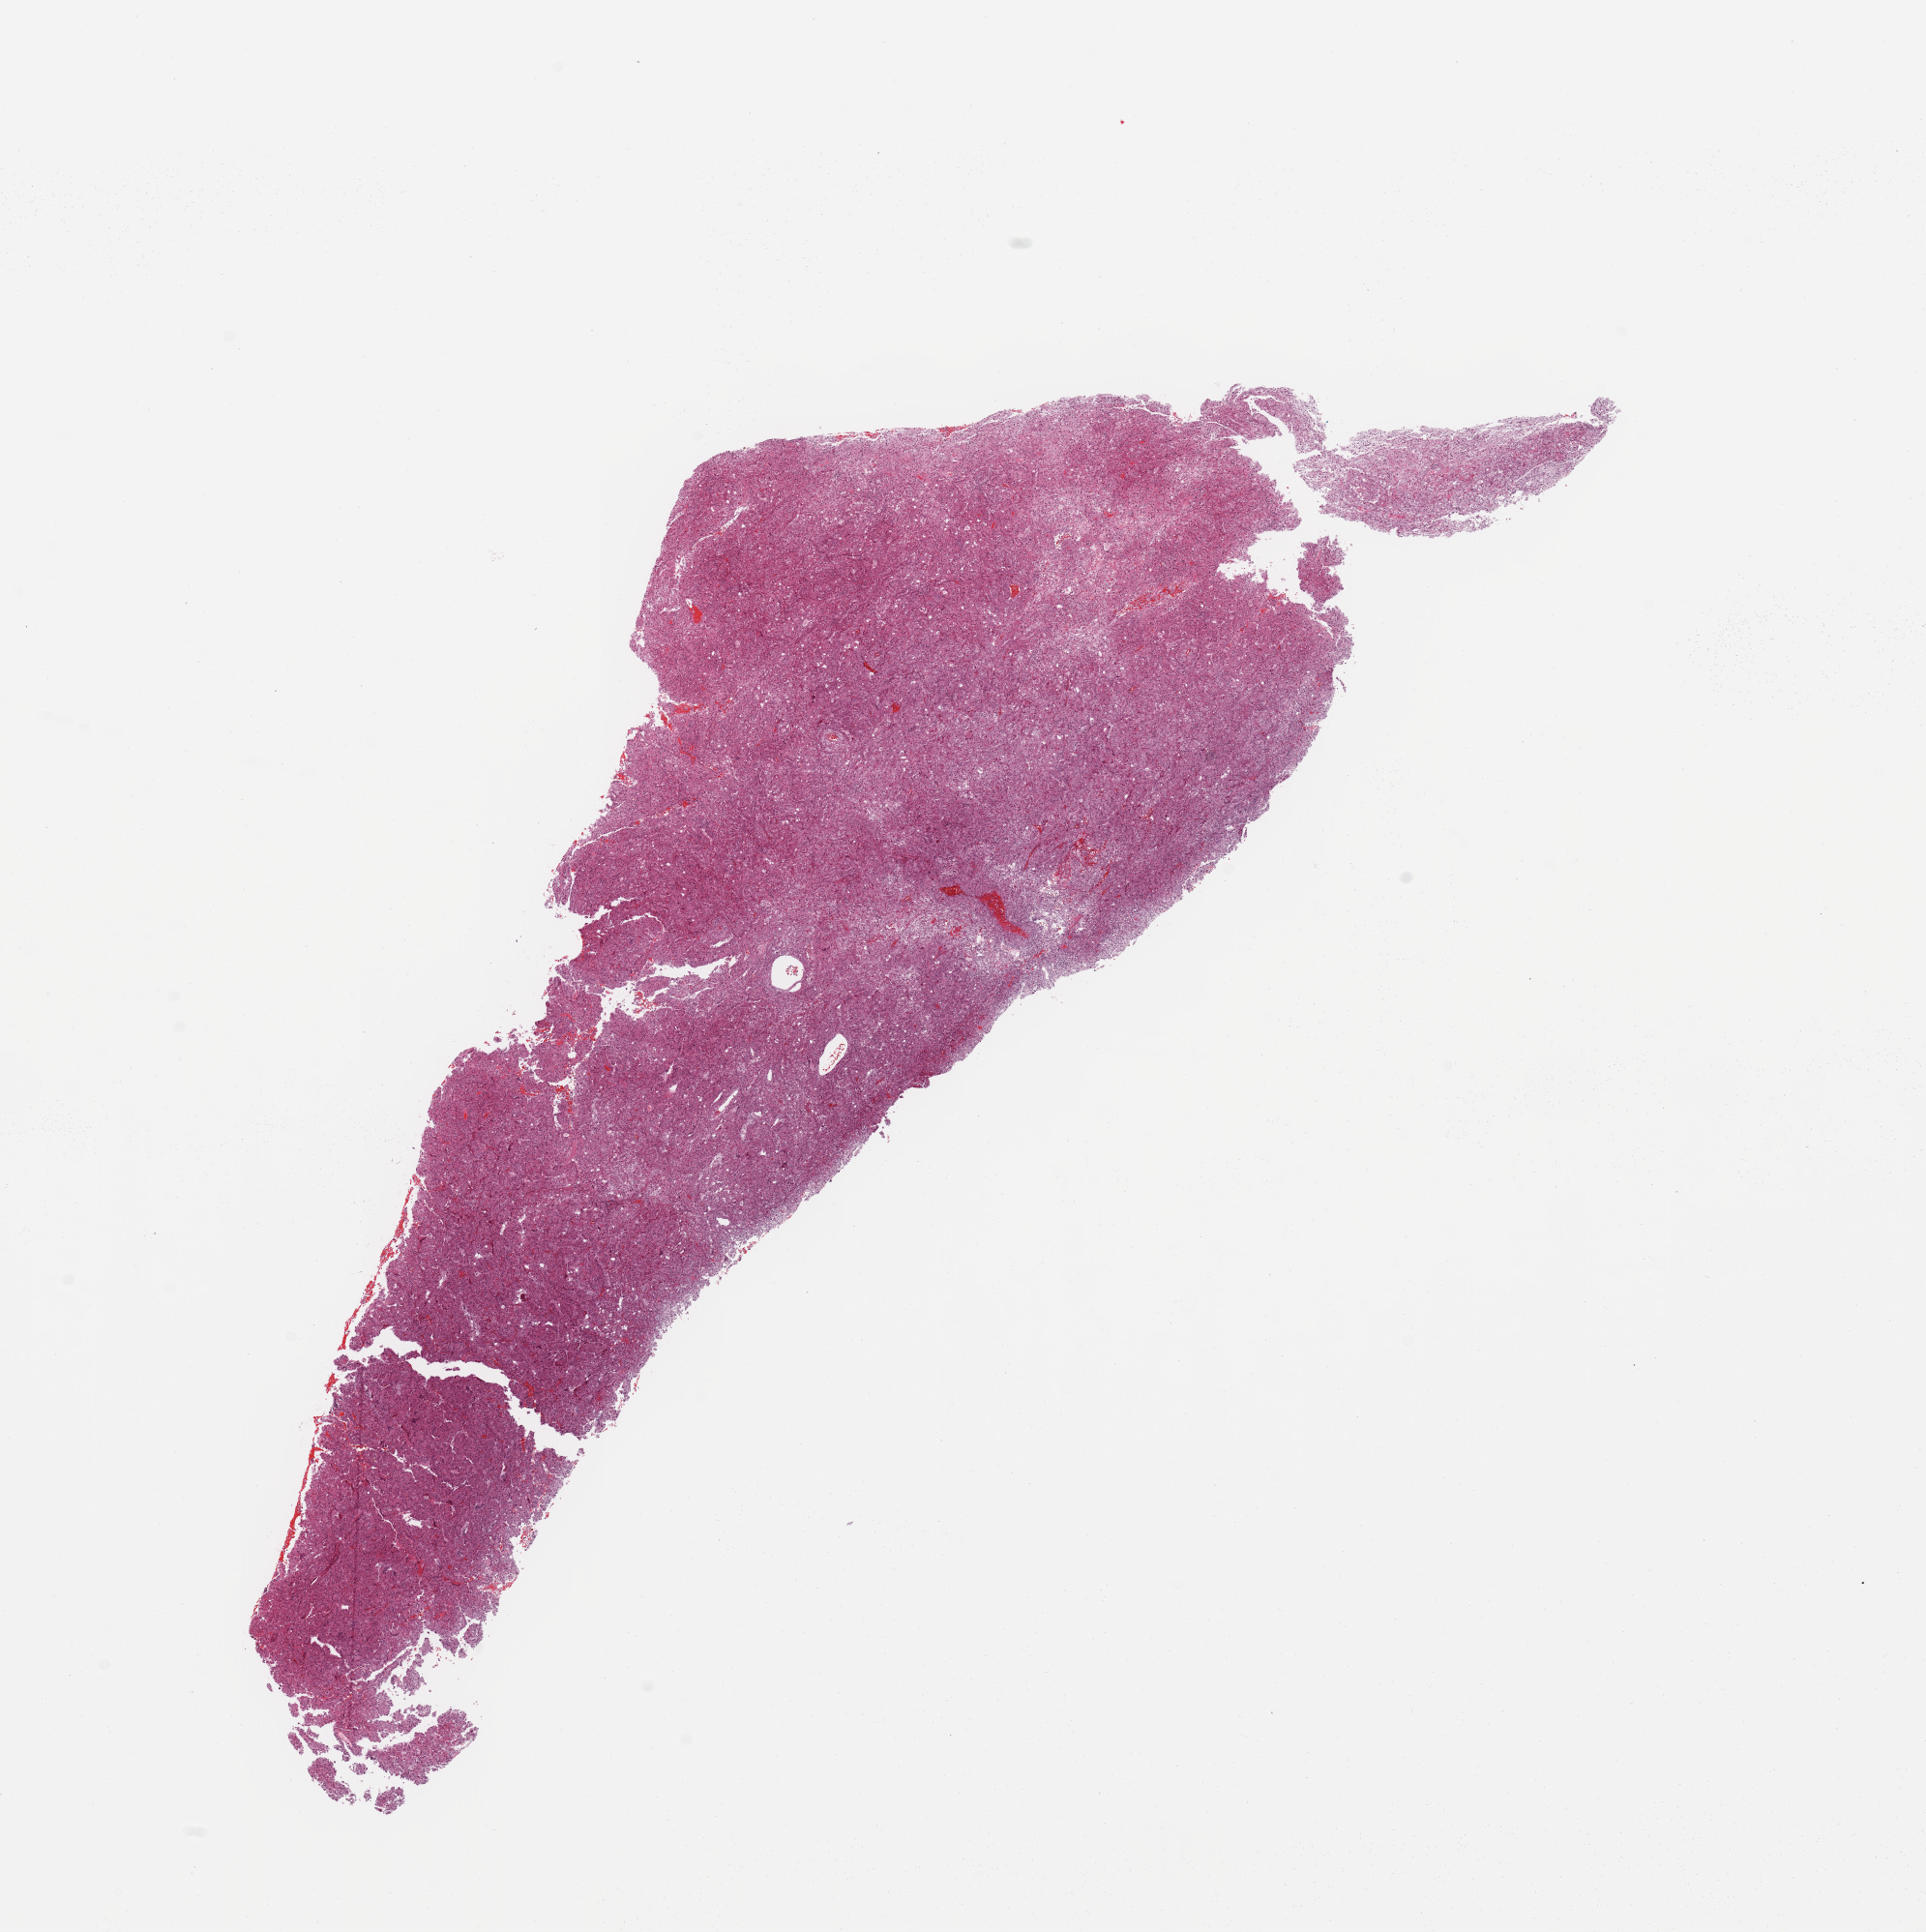
H&E whole-slide image — whole scanned area (about 15.8 x 15.8 mm, acquisition: 20x scan) shown as a low-resolution overview. Kidney, tumour tissue. 68-year-old female patient. Histologic grade: G4 (undifferentiated).
- diagnosis: Renal cell carcinoma, NOS
- primary tumour site (as recorded): middle
- AJCC pathologic stage: I